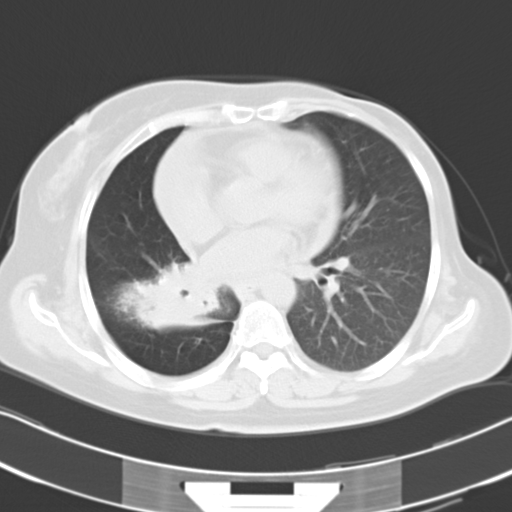
Chest CT, one axial slice; position 15 of 30 along the scan axis; lung window (W 1500 / L -600 HU); 8 mm slice thickness; 512 × 512 image matrix, field of view 331 × 331 mm. Patient: female, 53 years. From the clinical record (not read from this slice): clinical TNM (as recorded): T2b N1 M0.
Outlined on this slice (bounding box drawn by a radiologist):
- lung tumour (recorded histology: adenocarcinoma): bounding box <126,258,221,330> (left, top, right, bottom; pixels)